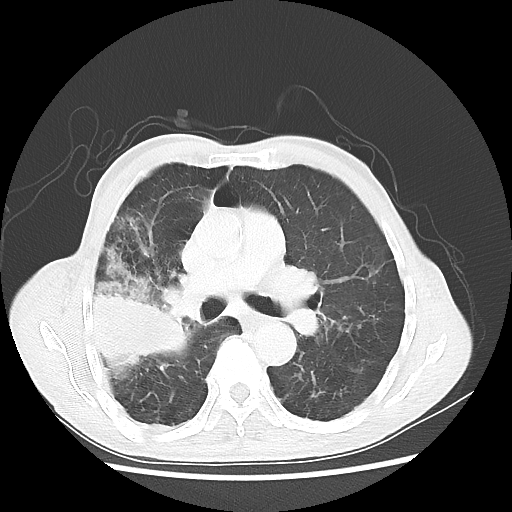
Chest CT, one axial slice; slice 31 of 58 in the series (ordered by position); 100 kVp; lung window (W 1500 / L -600 HU); 512 × 512 image matrix, field of view 351 × 351 mm. Patient: male, 75 years. From the clinical record (not read from this slice): clinical TNM (as recorded): T4 N1 M1.
Outlined on this slice (bounding box drawn by a radiologist):
- lung tumour (recorded histology: adenocarcinoma): bounding box (x1, y1, x2, y2) in pixels: (83, 270, 193, 376)